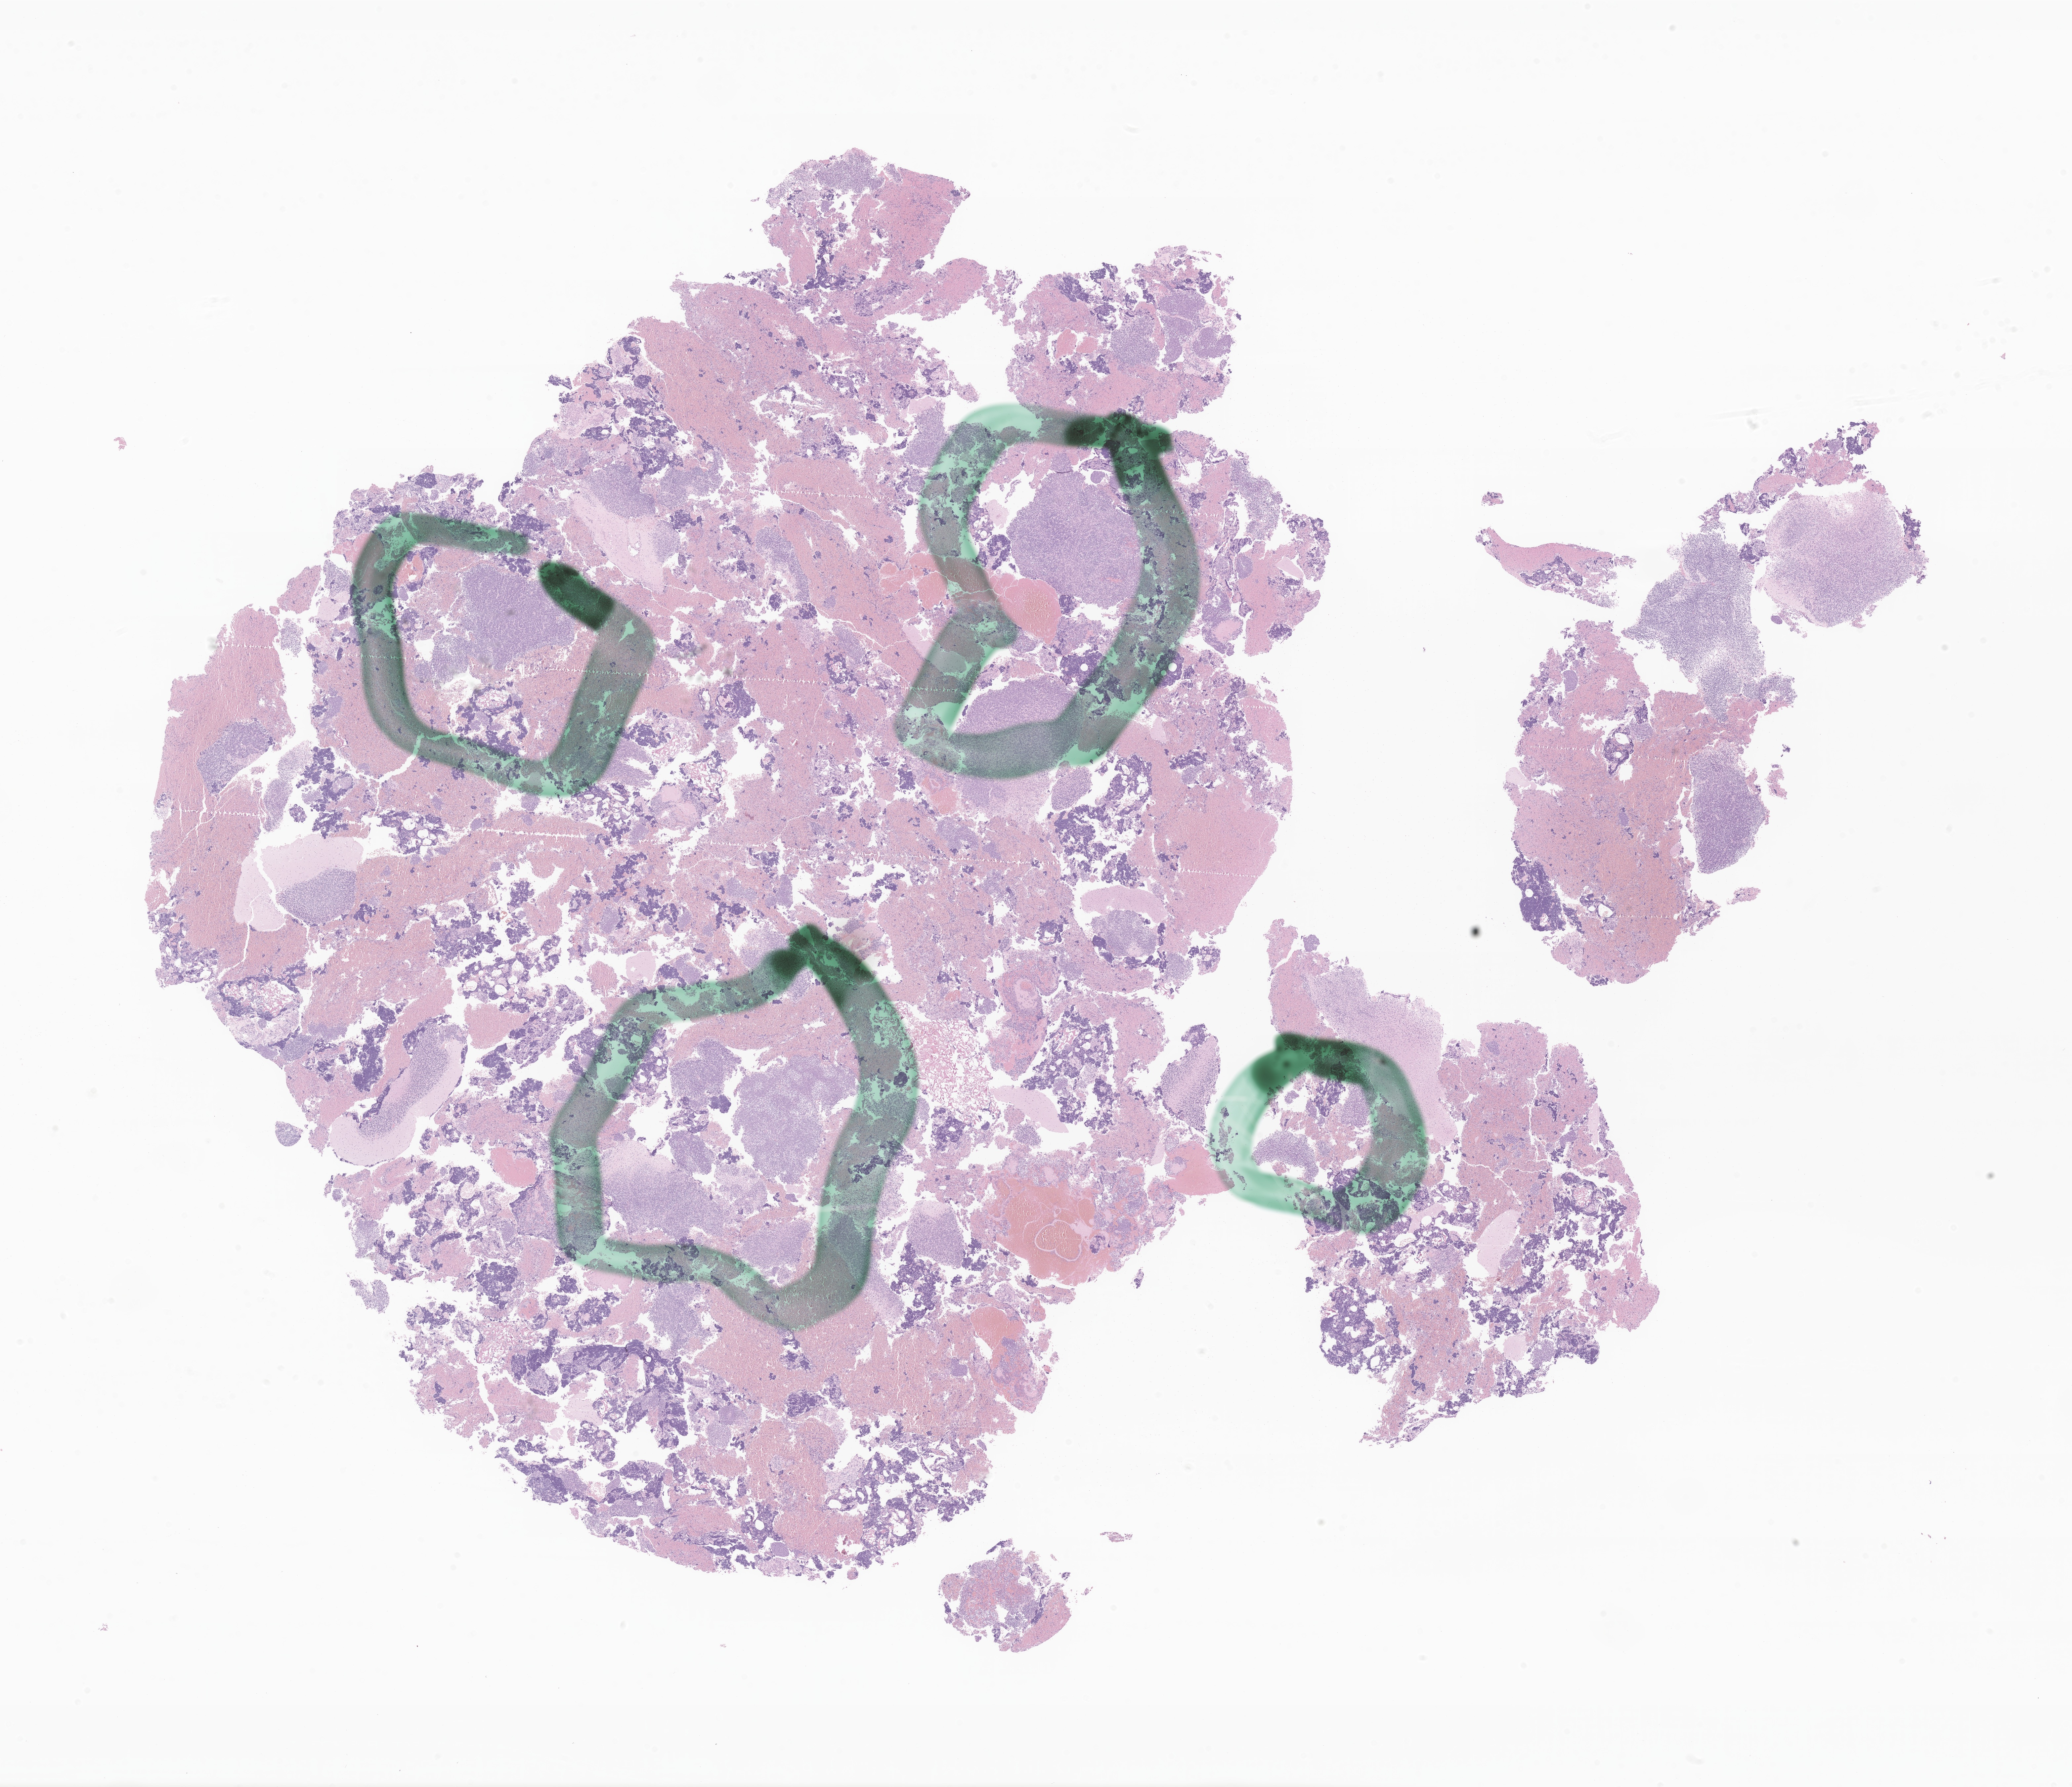
Whole-slide image, haematoxylin and eosin stain of tumor tissue from the brain, shown as a low-resolution overview of the whole scanned area (about 26.4 x 22.8 mm), FFPE section. Patient male; age 97 months (8 years 1 month).
Diagnosis (ICD-O-3 morphology term): Medulloblastoma, NOS.